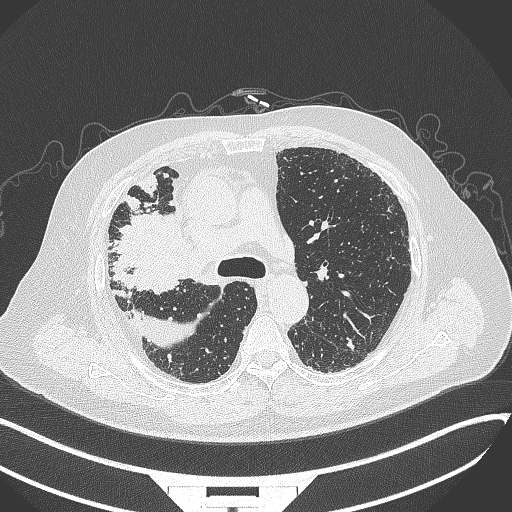
Chest CT, one axial slice. 120 kVp. Lung window (W 1500 / L -600 HU). 1 mm slice thickness. 512 × 512 image matrix, field of view 400 × 400 mm. Male patient, age 69 years. Case-level facts recorded for this patient, not image findings: clinical TNM (as recorded): T4 N3 M1.
Annotated regions visible in this slice (bounding box drawn by a radiologist):
- lung tumour (recorded histology: adenocarcinoma): box from (x=115, y=214) to (x=197, y=300) px